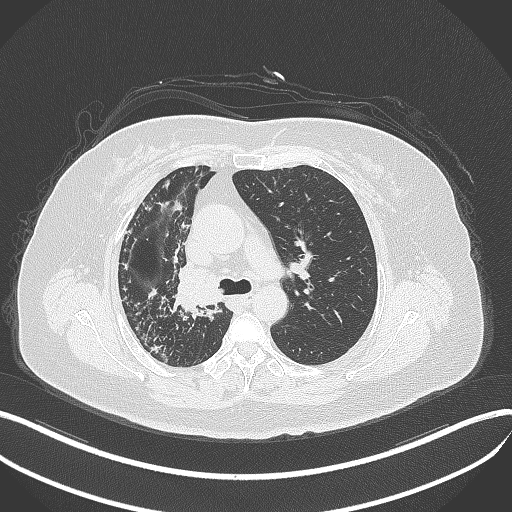
Chest CT, one axial slice. Position 238 of 376 along the scan axis. 120 kVp. Lung window (W 1500 / L -600 HU). 1 mm slice thickness. 512 × 512 image matrix, field of view 400 × 400 mm. Female patient, age 60 years. Case-level facts recorded for this patient, not image findings: clinical TNM (as recorded): T1c N0 M0.
Outlined on this slice (bounding box drawn by a radiologist):
- lung tumour (recorded histology: squamous cell carcinoma): bounding box [x1, y1, x2, y2] px = [170, 260, 226, 314]